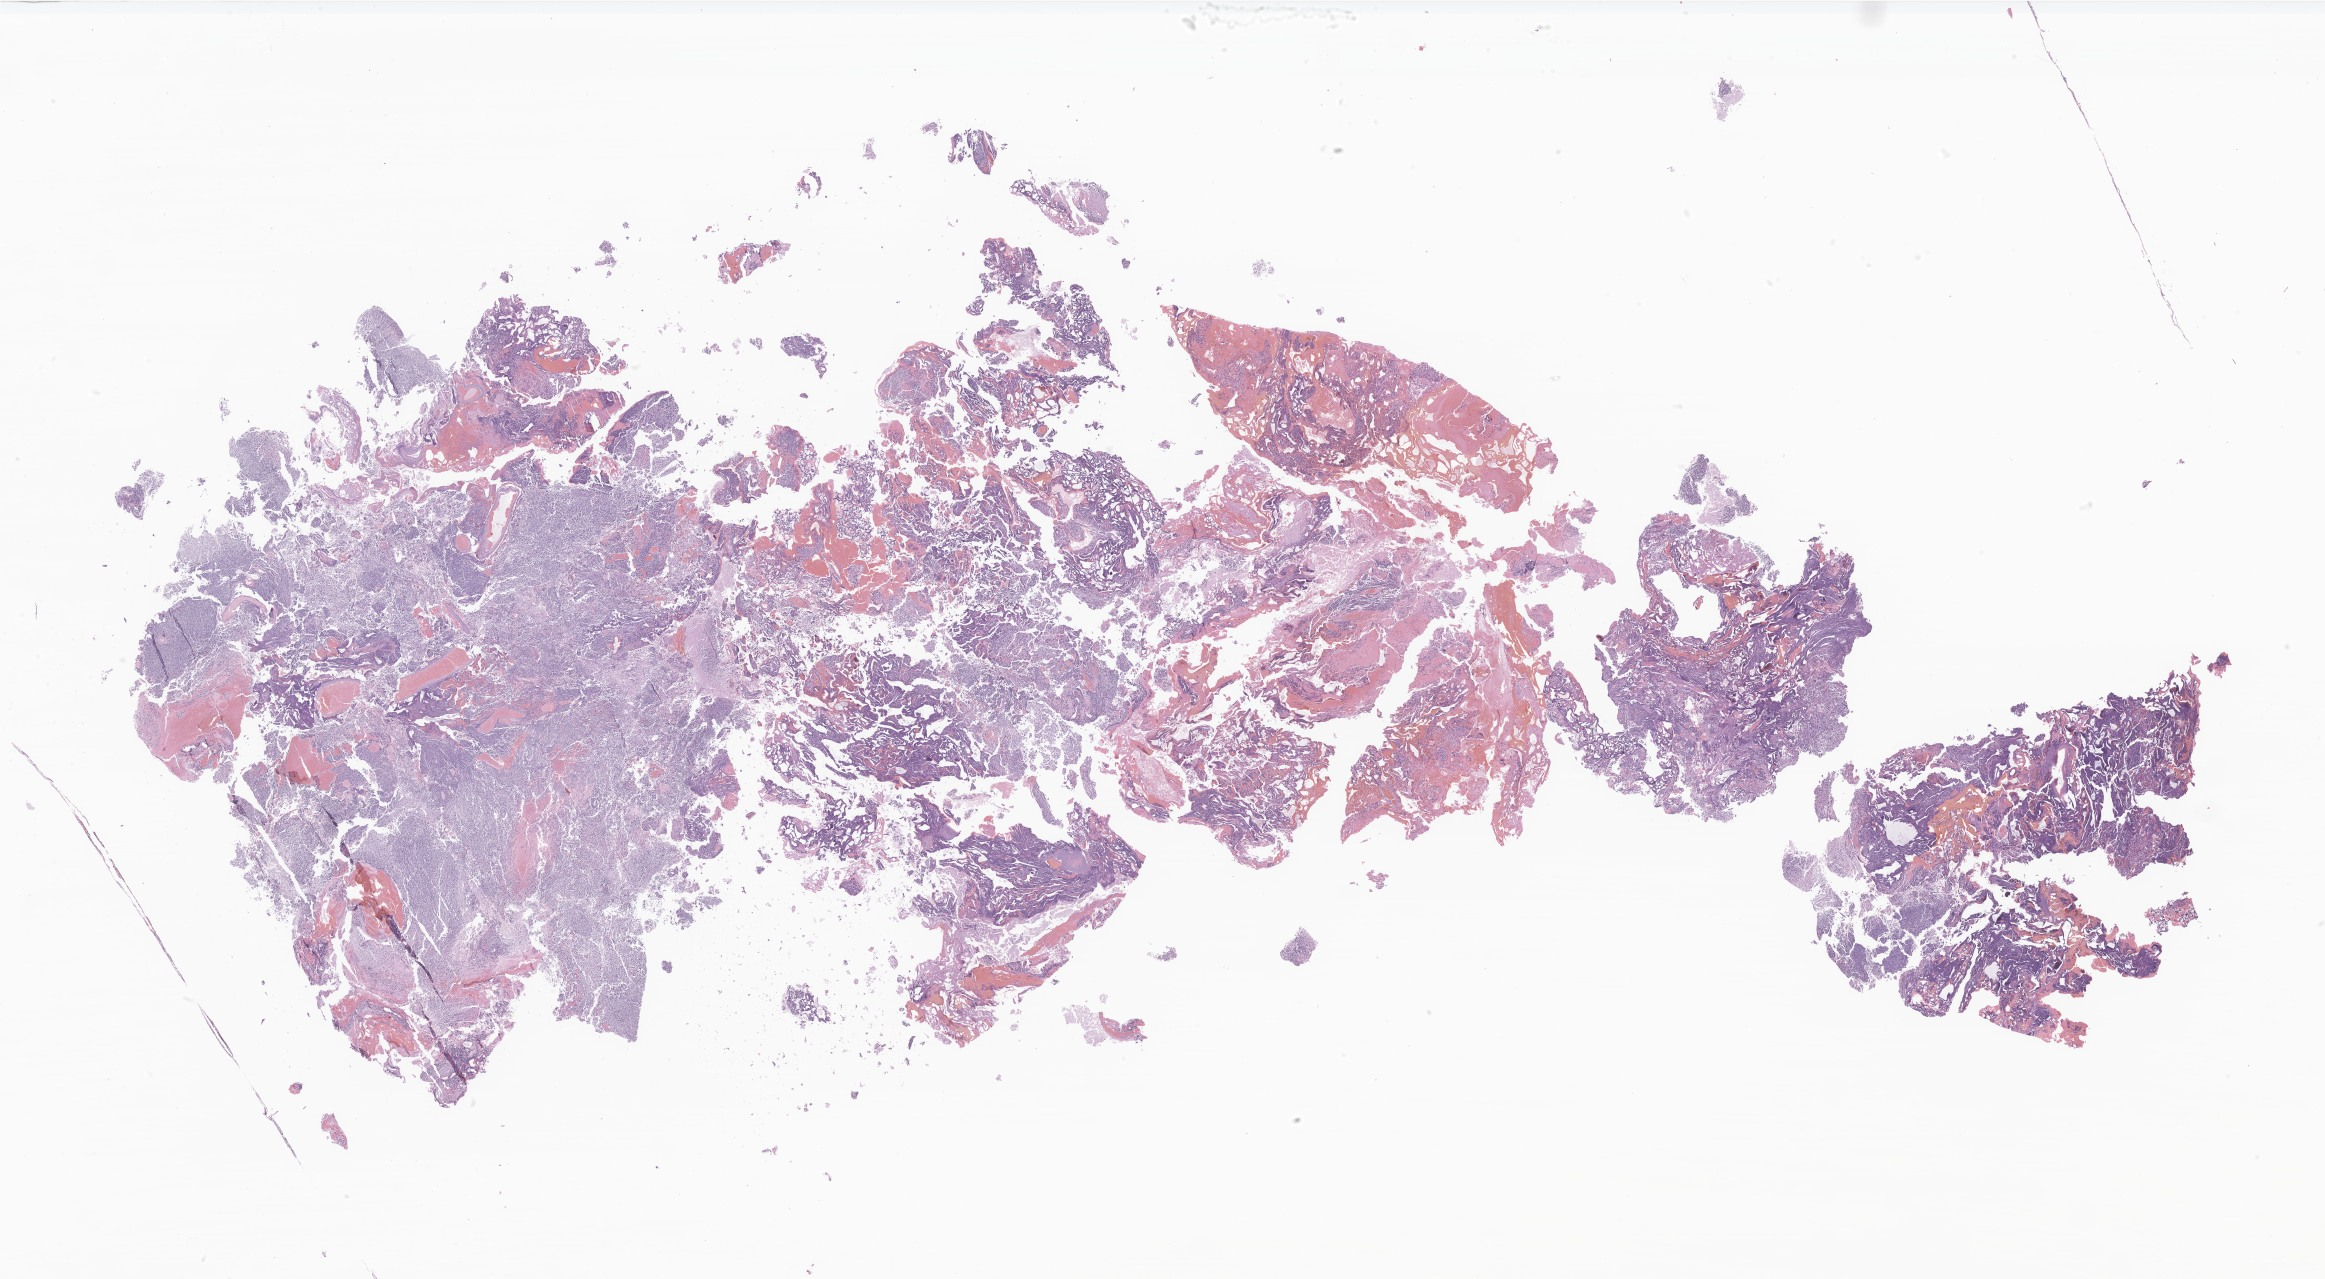
Whole-slide image, H&E stain of tumor tissue from the brain, a low-resolution overview of the entire scanned area, about 39.2 x 21.6 mm, formalin-fixed, paraffin-embedded (FFPE) tissue. Male patient, age 123 months (10 years 3 months).
- recorded diagnosis: Medulloblastoma, NOS